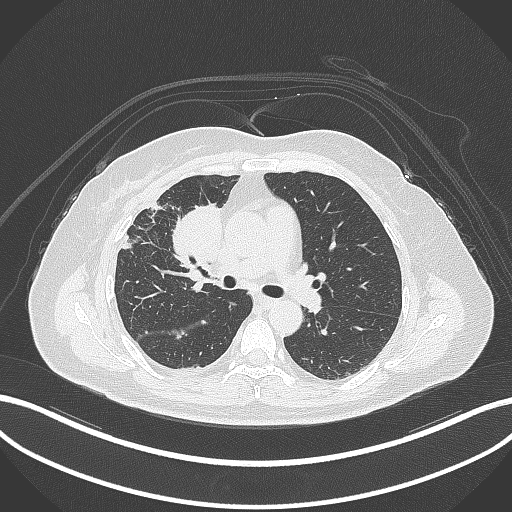
Chest CT, one axial slice; slice 167 of 305 in the series (ordered by position); reconstruction kernel B70f; lung window (W 1500 / L -600 HU); 1 mm slice thickness; 512 × 512 image matrix, field of view 400 × 400 mm. Patient: female, 52 years. Case-level facts recorded for this patient, not image findings: clinical TNM (as recorded): T3 N1 M1.
Outlined on this slice (bounding box drawn by a radiologist):
- lung tumour (recorded histology: adenocarcinoma): bounding box [x1, y1, x2, y2] px = [169, 199, 224, 275]